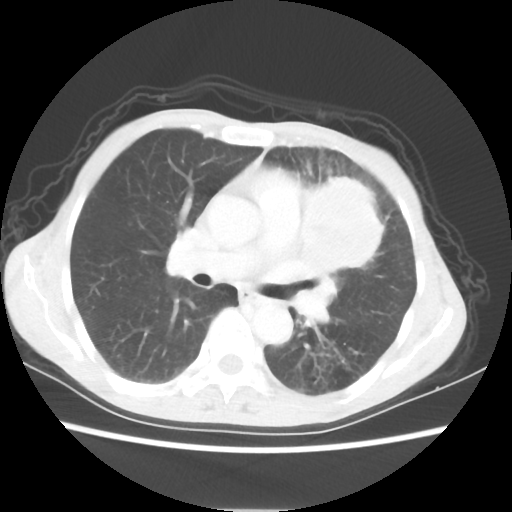
Chest CT, one axial slice. Slice 34 of 56 in the series (ordered by position). 80 kVp. Lung window (W 1500 / L -600 HU). 512 × 512 image matrix, field of view 331 × 331 mm. Patient: female, 60 years. From the clinical record (not read from this slice): clinical TNM (as recorded): T4 N1 M0.
Annotated regions visible in this slice (rectangle marked by the reading radiologist):
- lung tumour (recorded histology: adenocarcinoma): bounding box (x1, y1, x2, y2) in pixels: (292, 174, 388, 279)